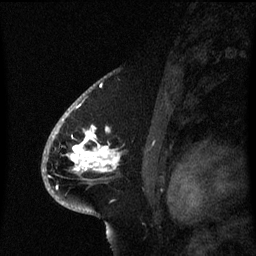
Breast MRI (dynamic contrast-enhanced), one sagittal slice; dynamic contrast-enhanced series, image 2 of 3 at this slice position (ordered by acquisition); 1.5 T; TE 4.2 ms, TR 8.4 ms; 2.1 mm slice thickness; 256 × 256 image matrix, field of view 200 × 200 mm. Female patient, age 53 years. Case-level facts recorded for this patient, not image findings: setting: breast cancer imaged before/during neoadjuvant chemotherapy; receptor status: HR-positive, HER2-negative.
Annotated regions visible in this slice (semi-automatically segmented with operator editing):
- analysis volume of interest (the breast-tissue region the enhancement analysis was run in; not a lesion): bounding box (x1, y1, x2, y2) in pixels: (49, 108, 124, 201)
- tumour enhancement mask (voxels above the 70 % enhancement threshold inside the analysis volume of interest): (53, 132, 120, 173)